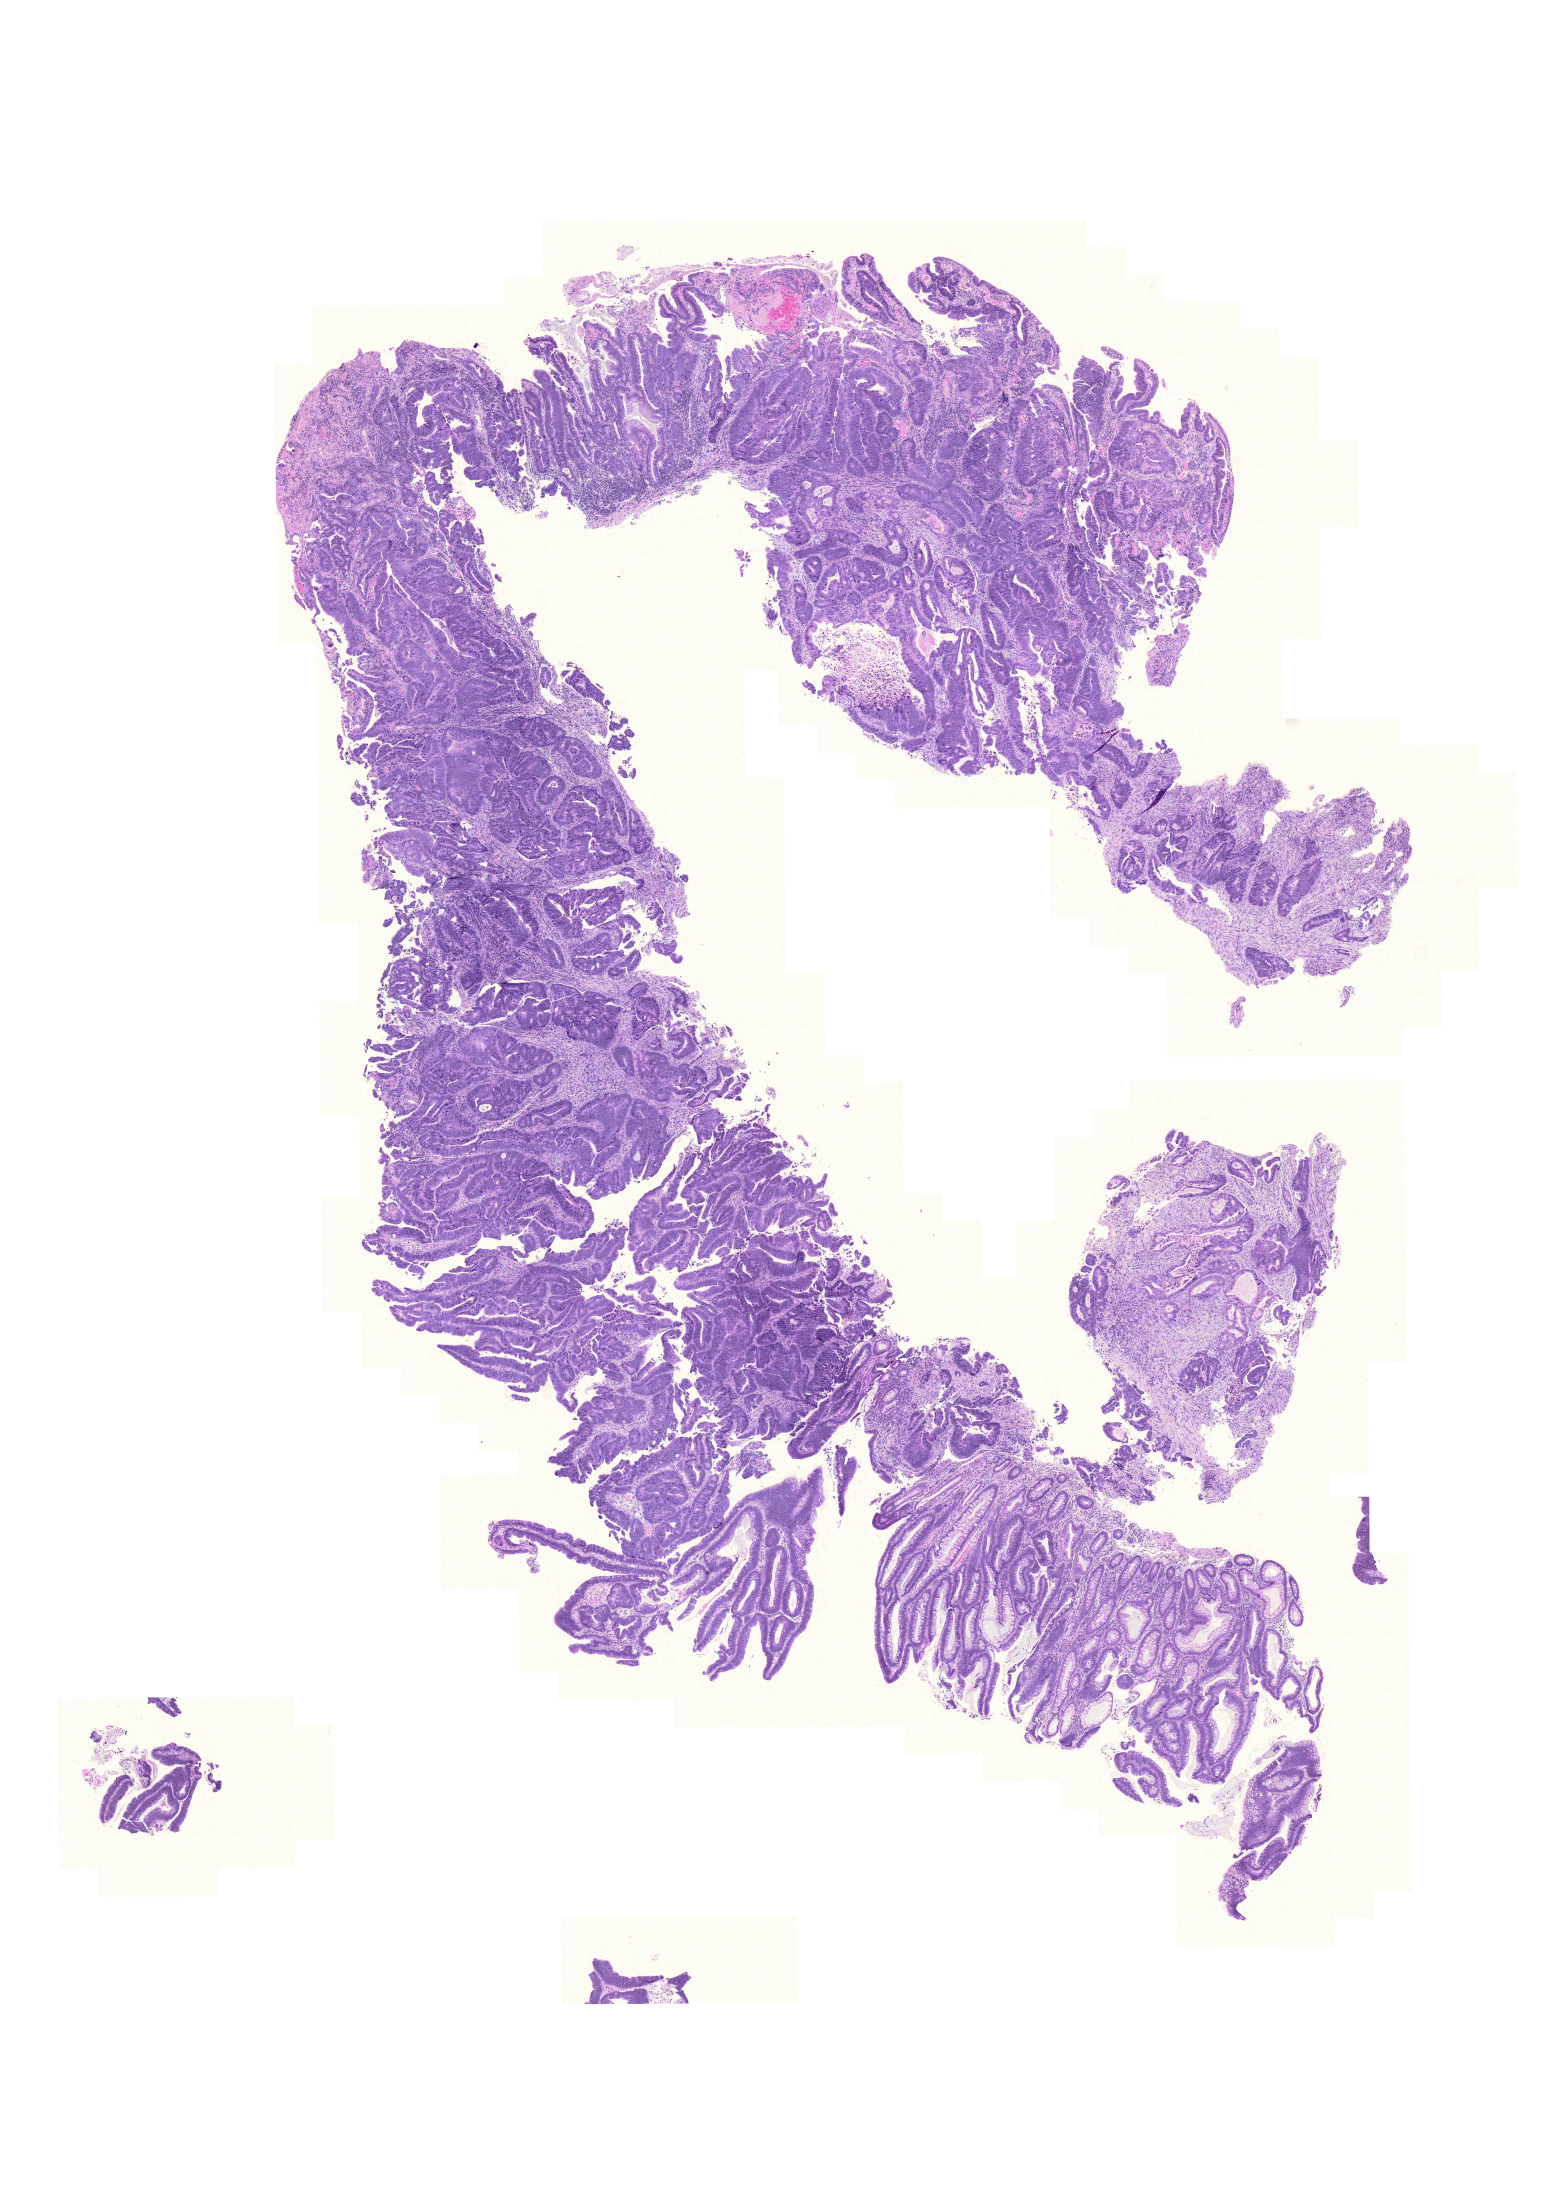
H&E-stained whole-slide image, whole scanned area (about 11.5 x 16.4 mm, from a 20x scan) shown as a low-resolution overview; formalin-fixed paraffin-embedded (FFPE) diagnostic section; colon, primary tumour sample. Female, age 82 years at initial diagnosis.
Diagnosis: Adenocarcinoma, NOS. AJCC pathologic stage: IV. Lymph nodes positive (case pathology): 4 of 16 examined.